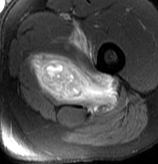
MRI of an extremity soft-tissue mass, one axial slice. Slice 60 of 70 in the series (ordered by position). T2-weighted fat-saturated. MR volume resampled by the dataset authors to the PET/CT grid (not the native acquisition matrix). 158 × 164 image matrix. Male patient. From the clinical record (not read from this slice): histological type: extraskeletal osteosarcoma; grade: high; site of the primary tumour: left adductur.
Structures marked on this image (expert contour drawn on MRI and transferred to this co-registered scan by the dataset authors):
- gross tumour volume (mass): box from (x=31, y=23) to (x=119, y=113) px